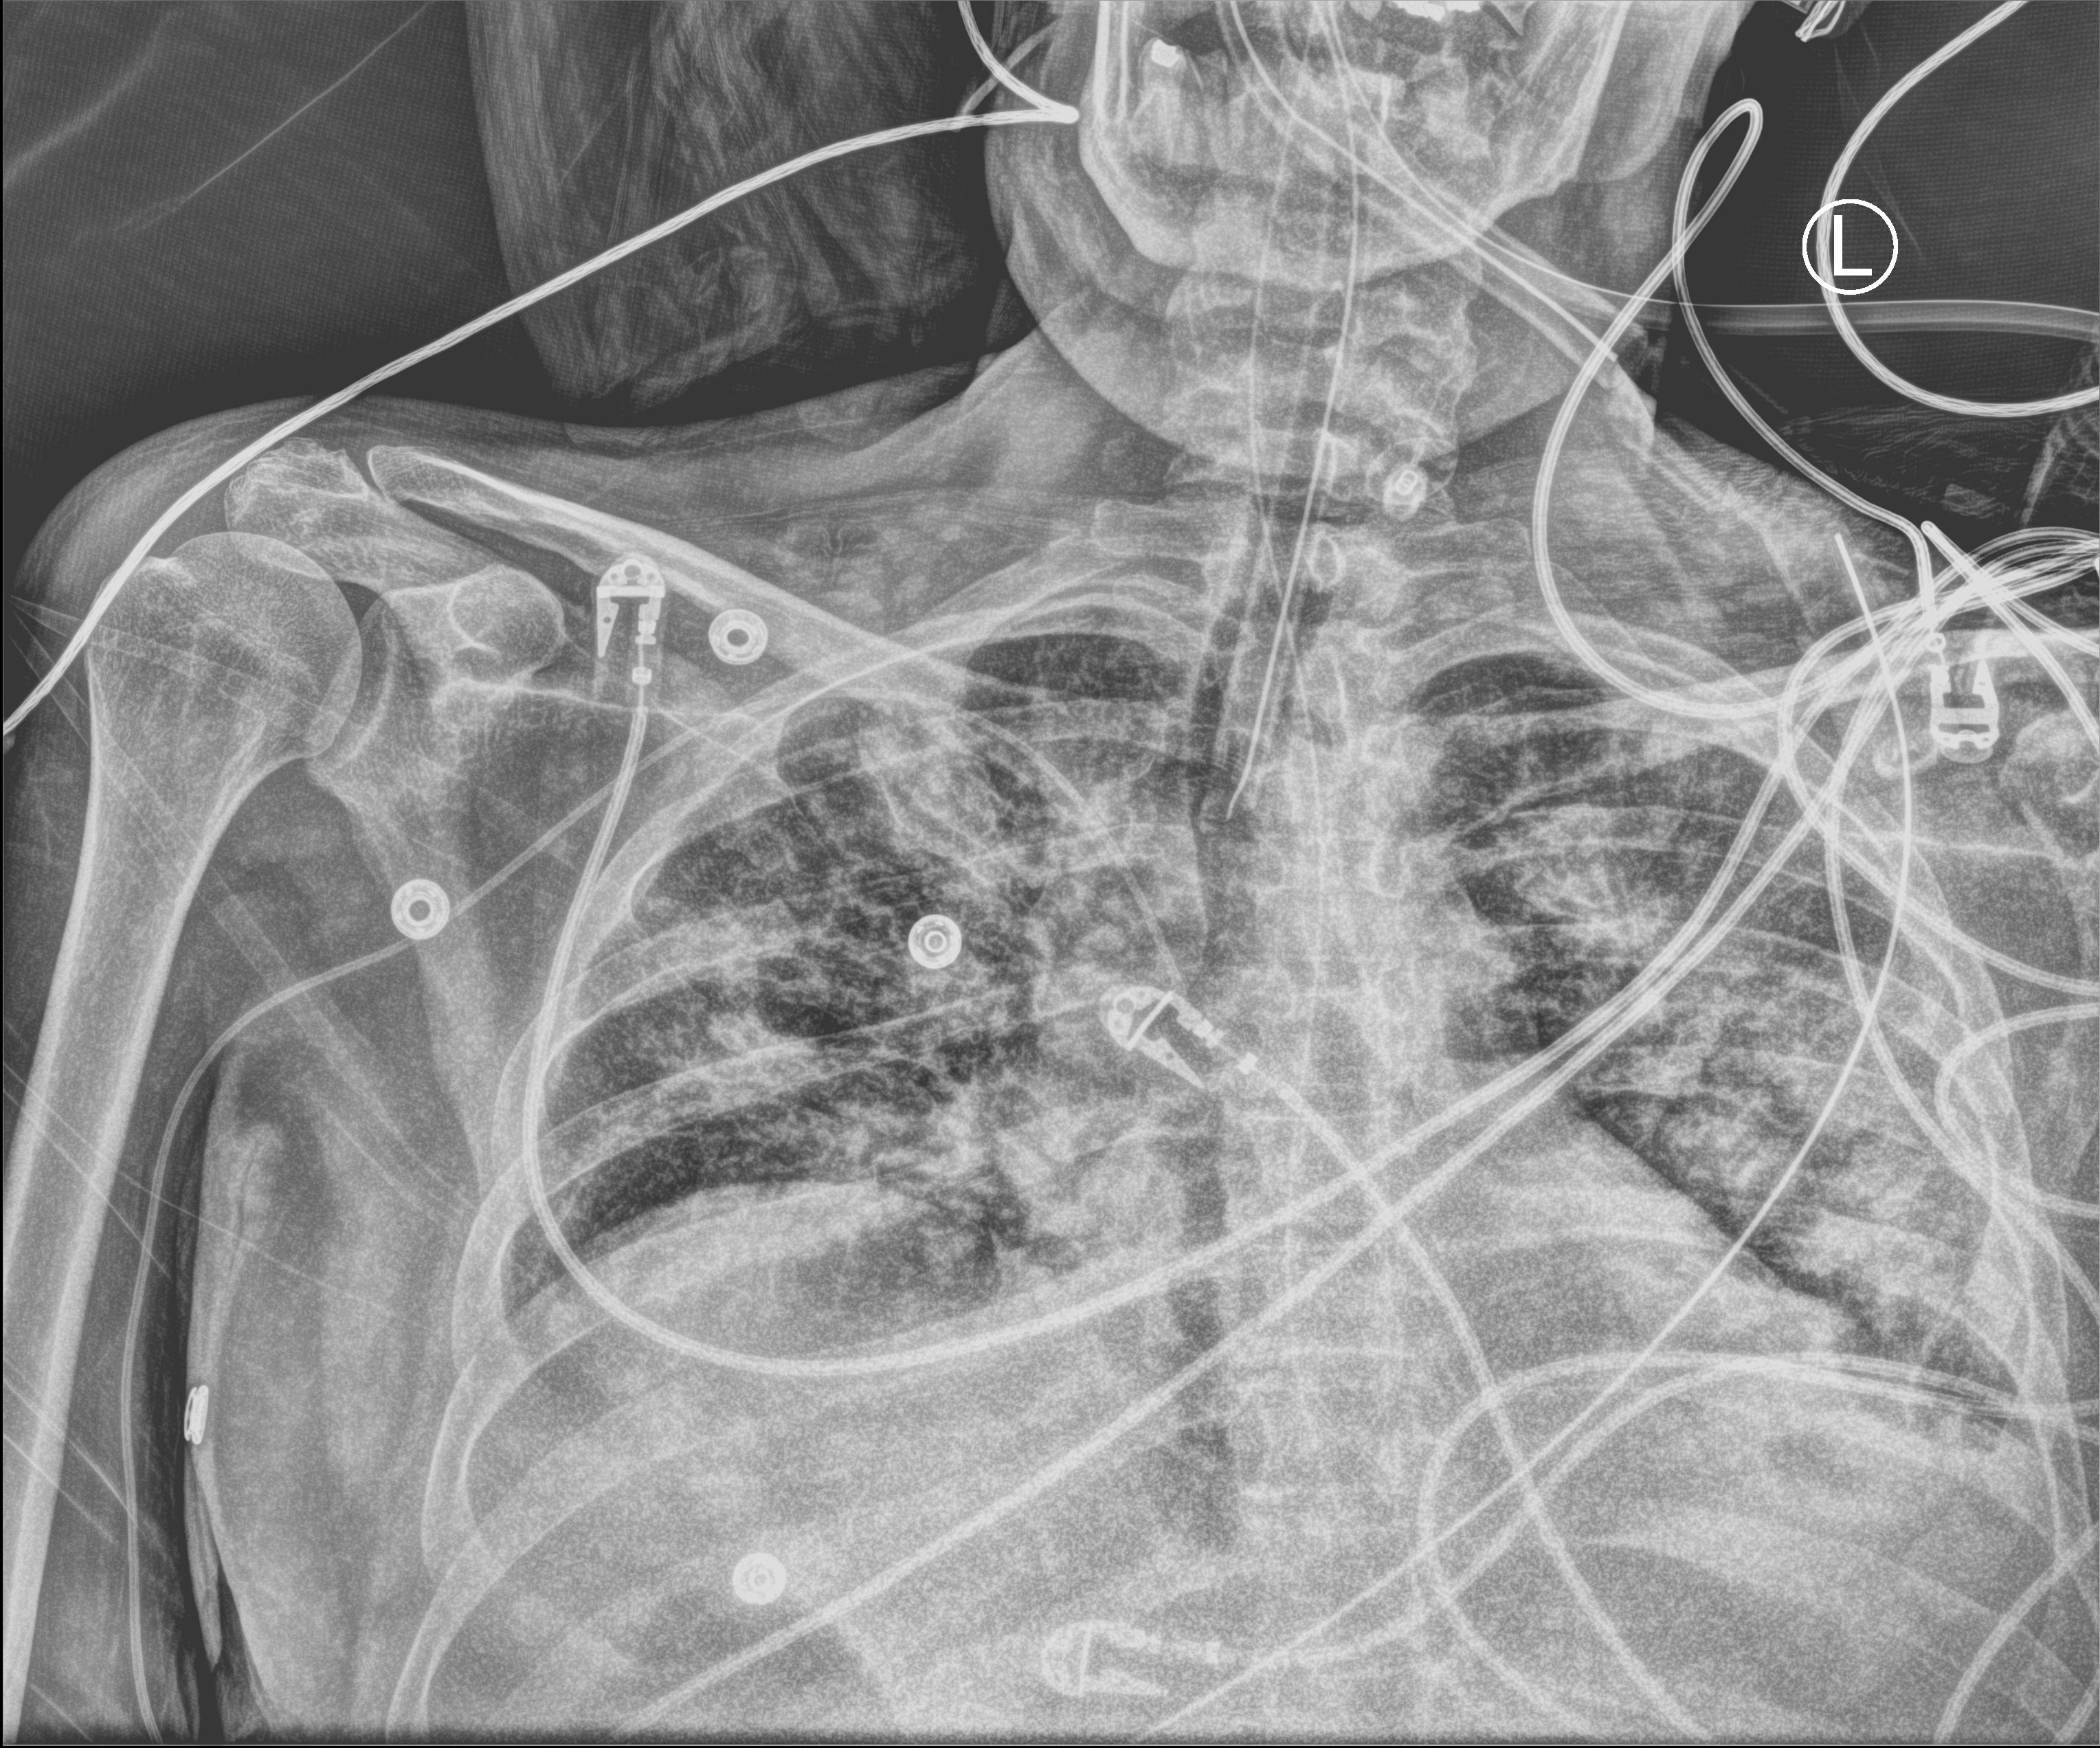
Chest X-ray (portable), anteroposterior (AP) projection. Male patient hospitalised with COVID-19, age 18–59 years.
Hospital-stay facts (about this admission, not read from this image; timing relative to this image not recorded): other chronic lung disease (admission record): no; COPD (admission record): no; mechanically ventilated during this hospital stay: yes.